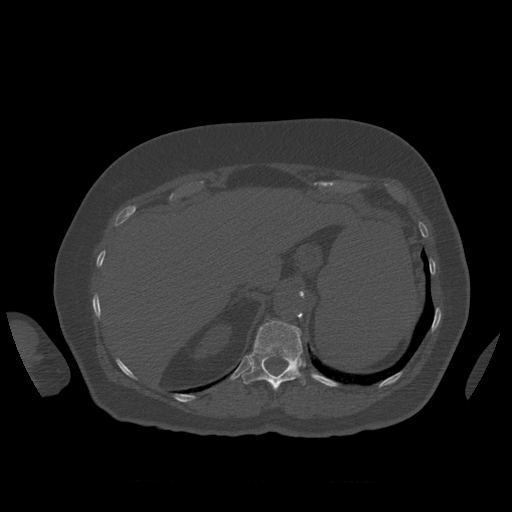
CT including the spine, one axial slice; position 302 of 399 along the scan axis; 120 kVp; bone window (W 1800 / L 400 HU); 1.25 mm slice thickness; 512 × 512 image matrix, field of view 404 × 404 mm. Patient age 81 years. Case-level facts recorded for this patient, not image findings: primary cancer: renal; vertebrae with lytic lesions (as recorded): L1.
Outlined on this slice (semi-automatically segmented with operator editing):
- T12 vertebra: bounding box <243,320,306,391> (left, top, right, bottom; pixels)